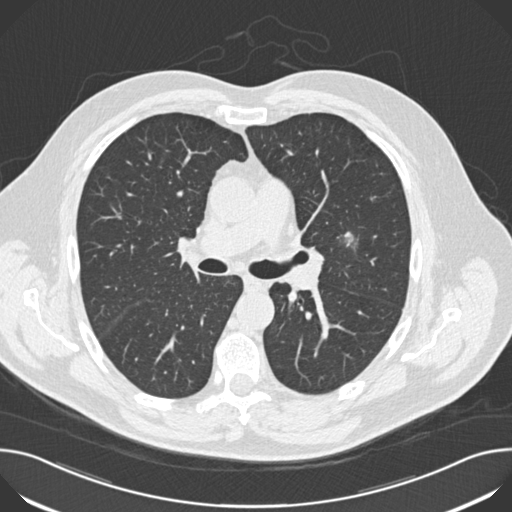
Low-dose screening chest CT, one axial slice. Slice 105 of 174 in the series (ordered by position). Lung window (W 1500 / L -600 HU). 512 × 512 image matrix, field of view 380 × 380 mm.
Annotated regions visible in this slice (expert manual segmentation):
- lesion 1 (tumor, upper lobe of left lung): bounding box (x1, y1, x2, y2) in pixels: (344, 232, 356, 247)